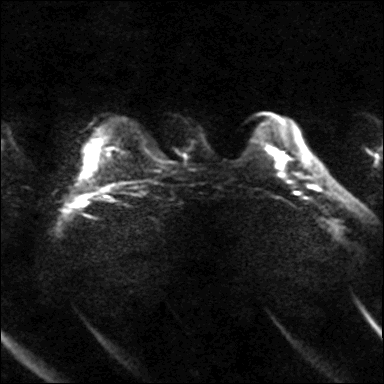
Breast MRI, one axial slice; slice 11 of 40 in the series (ordered by position); diffusion-weighted series; image 2 of 4 stored at this slice position (different b-values; order by instance number); 3 T; 384 × 384 image matrix, field of view 320 × 320 mm. Female patient.
Structures marked on this image (manually delineated by an expert):
- tumour on diffusion-weighted imaging: bounding box <279,154,284,162> (left, top, right, bottom; pixels)